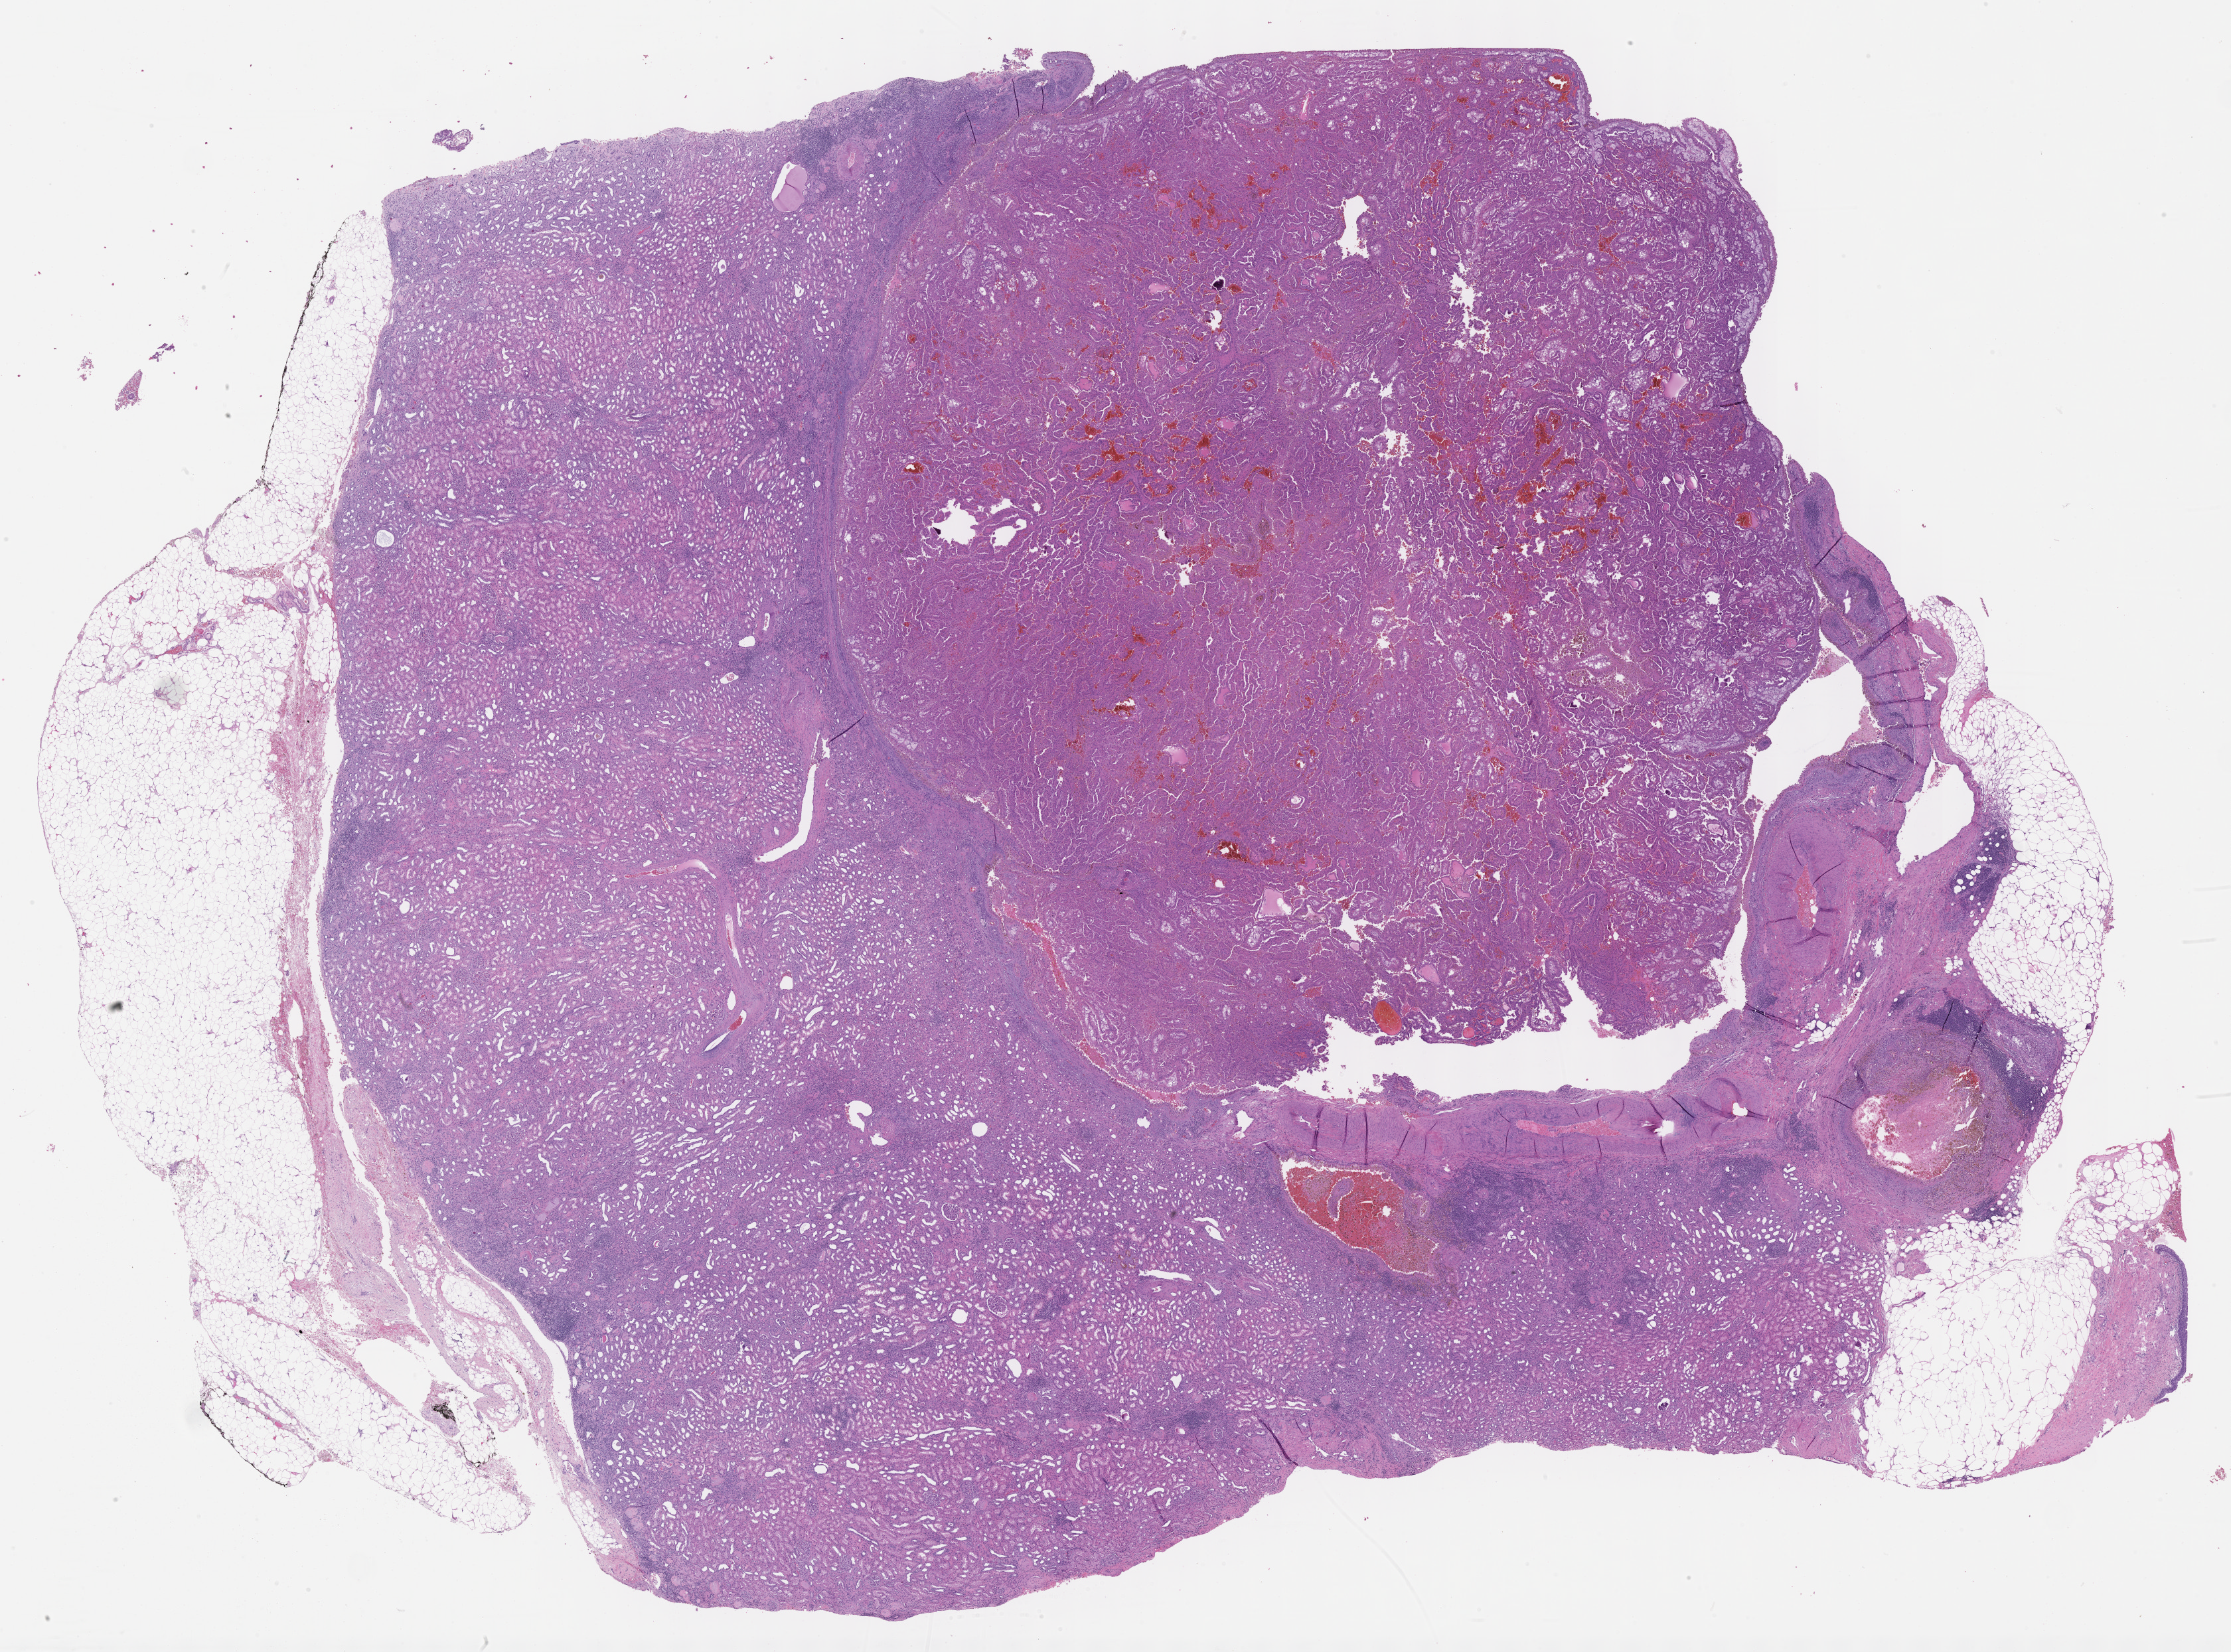
Whole-slide histology image, H&E-stained — low-resolution overview of the scanned area, about 27.2 x 20.1 mm, formalin-fixed paraffin-embedded (FFPE) diagnostic section, primary tumour sample from the kidney. Patient: male, age at initial diagnosis 69 years.
TNM: T1a NX MX. Diagnosis: Papillary adenocarcinoma, NOS. AJCC pathologic stage: I (7th edition).